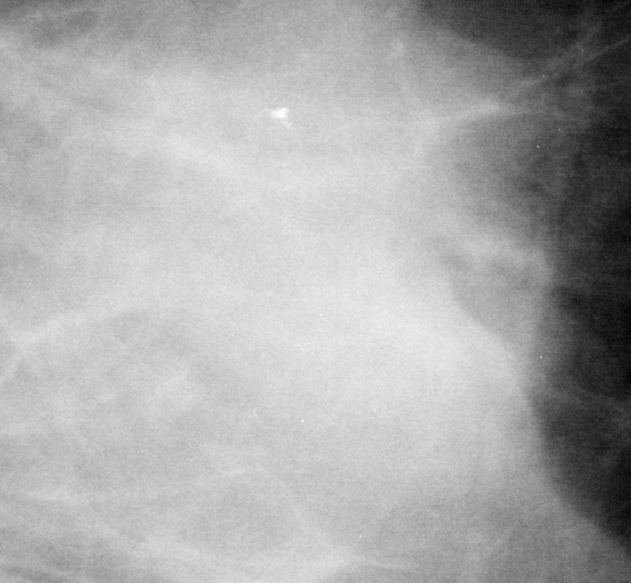
Cropped region of a digitized screen-film mammogram centred on a radiologist-marked abnormality, left breast, MLO view, BI-RADS breast density category 2 (scale 1–4).
- Finding: mass, shape round, margins ill defined; BI-RADS assessment category 4; pathology result (as recorded, not read from the image): malignant.